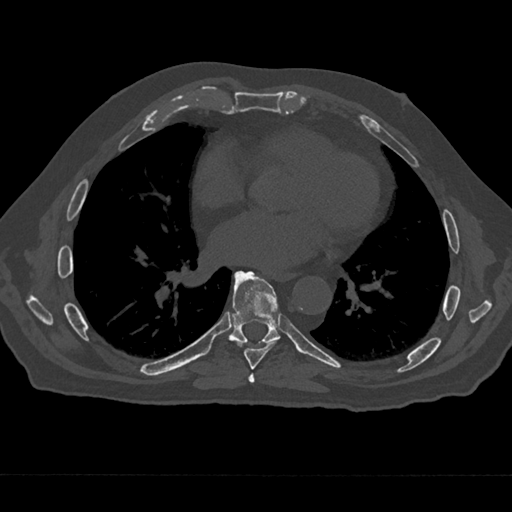
CT including the spine, one axial slice; position 344 of 797 along the scan axis; reconstruction kernel Br40s/3; 120 kVp; bone window (W 1800 / L 400 HU); 0.5 mm slice thickness; 512 × 512 image matrix, field of view 377 × 377 mm. Patient: male, 75 years. Case-level facts recorded for this patient, not image findings: primary cancer: renal.
Annotated regions visible in this slice (semi-automatic segmentation, software-assisted and operator-edited):
- T6 vertebra: box from (x=248, y=373) to (x=255, y=383) px
- T7 vertebra: (x=235, y=271)–(x=277, y=370)
- T8 vertebra: (x=229, y=271)–(x=280, y=344)